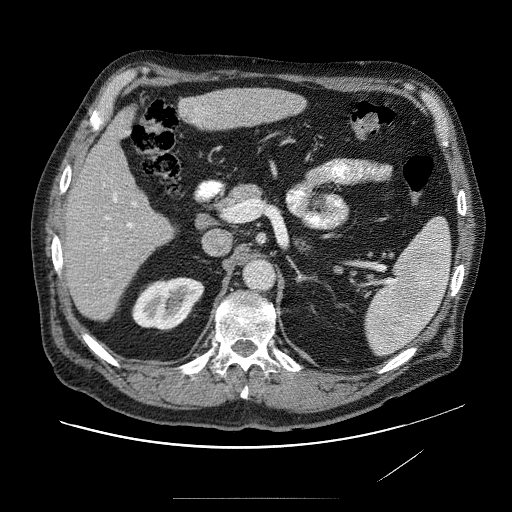
Contrast-enhanced abdominal CT (liver protocol), one axial slice; position 36 of 89 along the scan axis; reconstruction kernel STANDARD; 120 kVp; soft-tissue window (W 400 / L 40 HU); 2.5 mm slice thickness; 512 × 512 image matrix, field of view 420 × 420 mm. From the clinical record (not read from this slice): diagnosis: hepatocellular carcinoma (patient treated with transarterial chemoembolisation; whether this scan precedes or follows treatment is not stated here); TNM stage (as recorded): Stage-IVA; Child-Pugh class: A.
Outlined on this slice (semi-automatically segmented with operator editing):
- liver parenchyma outside the tumour (the mass and vessels are separate outlines, so this box may not span the whole liver): box from (x=62, y=85) to (x=312, y=324) px
- mass: (x=182, y=95)–(x=210, y=127)
- liver vessels: (x=86, y=104)–(x=253, y=281)